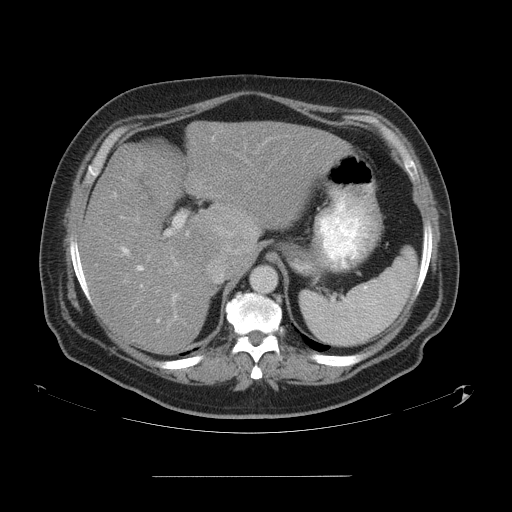
Contrast-enhanced abdominal CT, one axial slice; slice 38 of 58 in the series (ordered by position); 120 kVp; intravenous contrast given; soft-tissue window (W 400 / L 40 HU); 5 mm slice thickness; 512 × 512 image matrix. Male patient, age 63 years. From the clinical record (not read from this slice): diagnosis: colorectal cancer liver metastases, imaged before liver resection; multiple liver metastases: no; largest metastasis: 4.2 cm; disease in both lobes: no.
Annotated regions visible in this slice (manually delineated by an expert):
- hepatic veins: box from (x=113, y=192) to (x=226, y=321) px
- liver: (x=80, y=122)–(x=346, y=353)
- planned liver remnant (the part of the liver to remain after resection): (x=80, y=194)–(x=214, y=354)
- portal vein (with intrahepatic branches): (x=121, y=212)–(x=190, y=322)
- liver metastasis: (x=219, y=222)–(x=246, y=255)